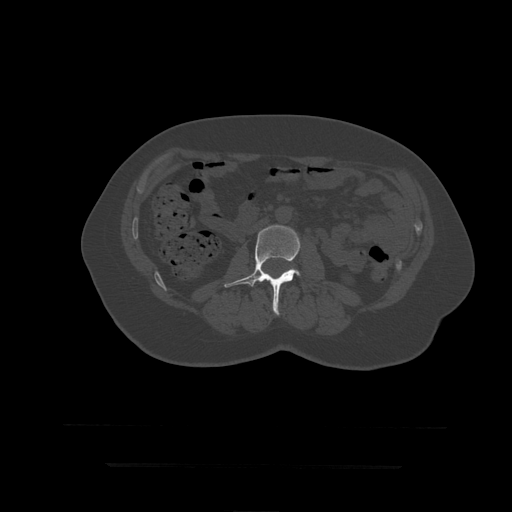
CT including the spine, one axial slice. Slice 124 of 399 in the series (ordered by position). Bone window (W 1800 / L 400 HU). 1.25 mm slice thickness. 512 × 512 image matrix, field of view 450 × 450 mm. Patient age 41 years. Case-level facts recorded for this patient, not image findings: primary cancer: breast.
Annotated regions visible in this slice (semi-automatically segmented with operator editing):
- L3 vertebra: bounding box [x1, y1, x2, y2] px = [225, 225, 301, 316]